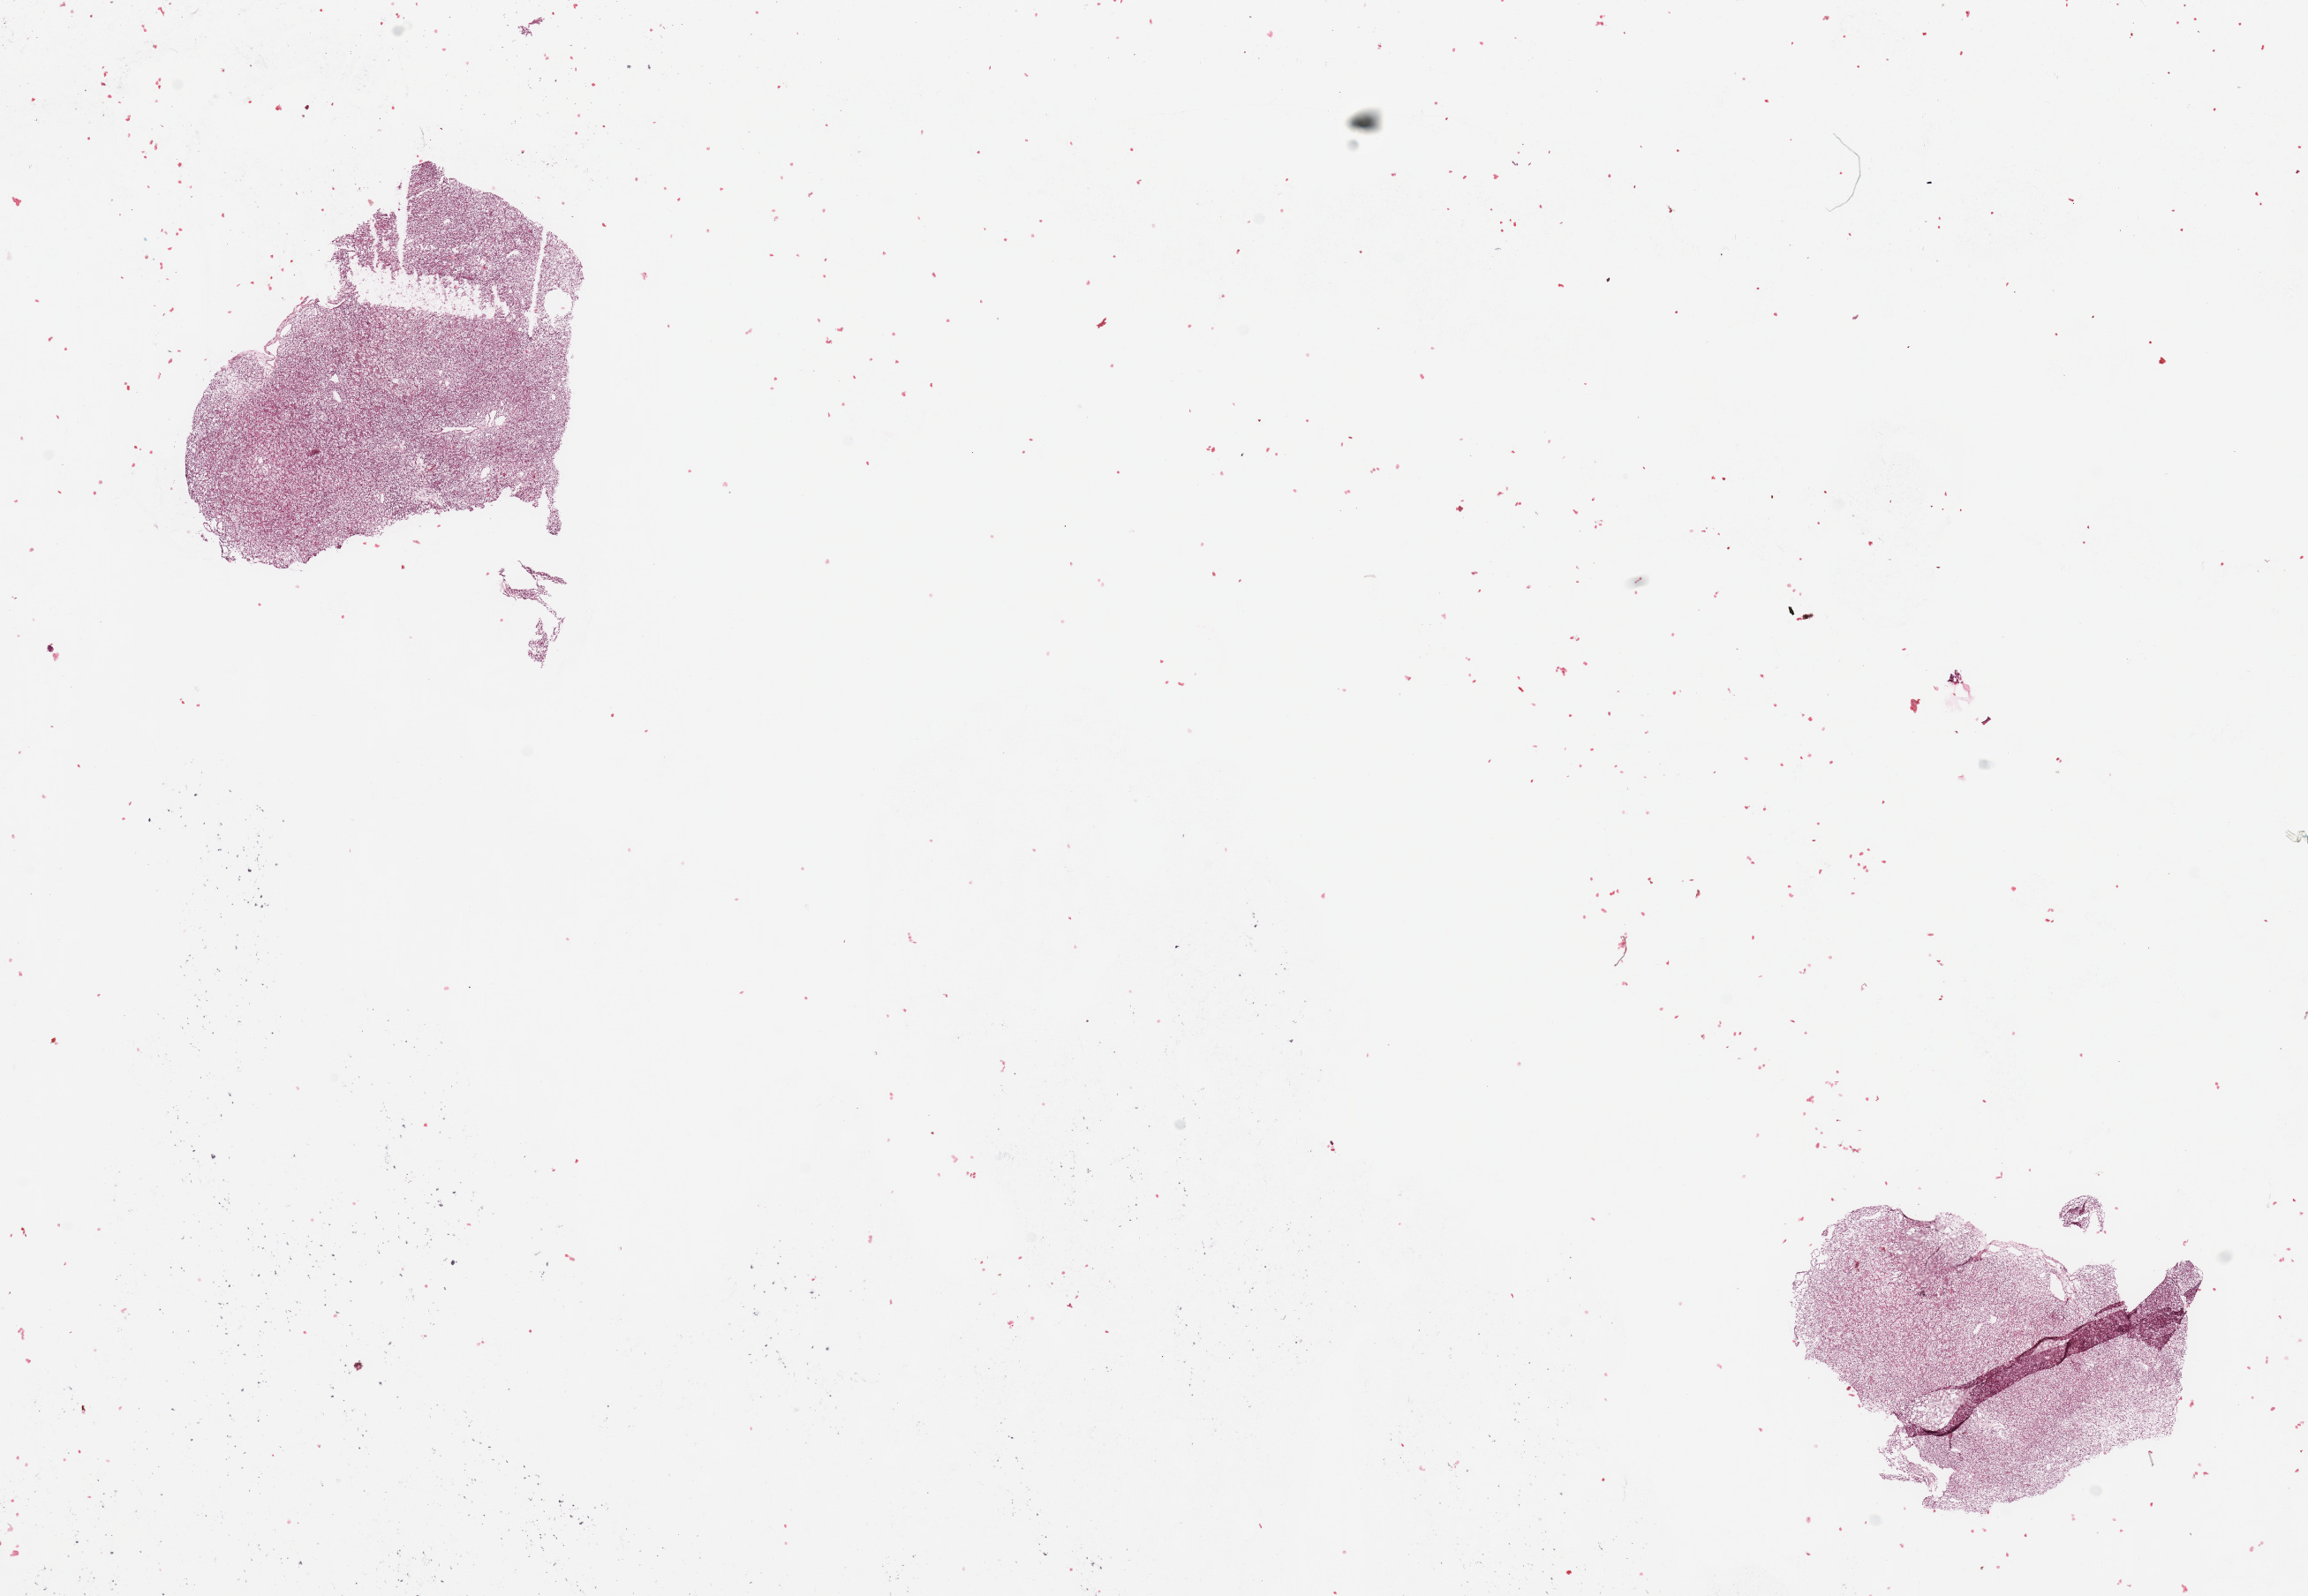
Hematoxylin and eosin (H&E) stained whole-slide image — shown as a low-resolution overview of the whole scanned area (about 20.7 x 14.3 mm); tumour tissue sample, sampled site: kidney. Male, 65 y/o. Histologic grade: G1 (well differentiated). Slide review estimates, as recorded: tumour nuclei 85%, necrosis 0%.
Diagnosis: Renal cell carcinoma, NOS. Primary tumour site (as recorded): middle. AJCC pathologic stage: I.